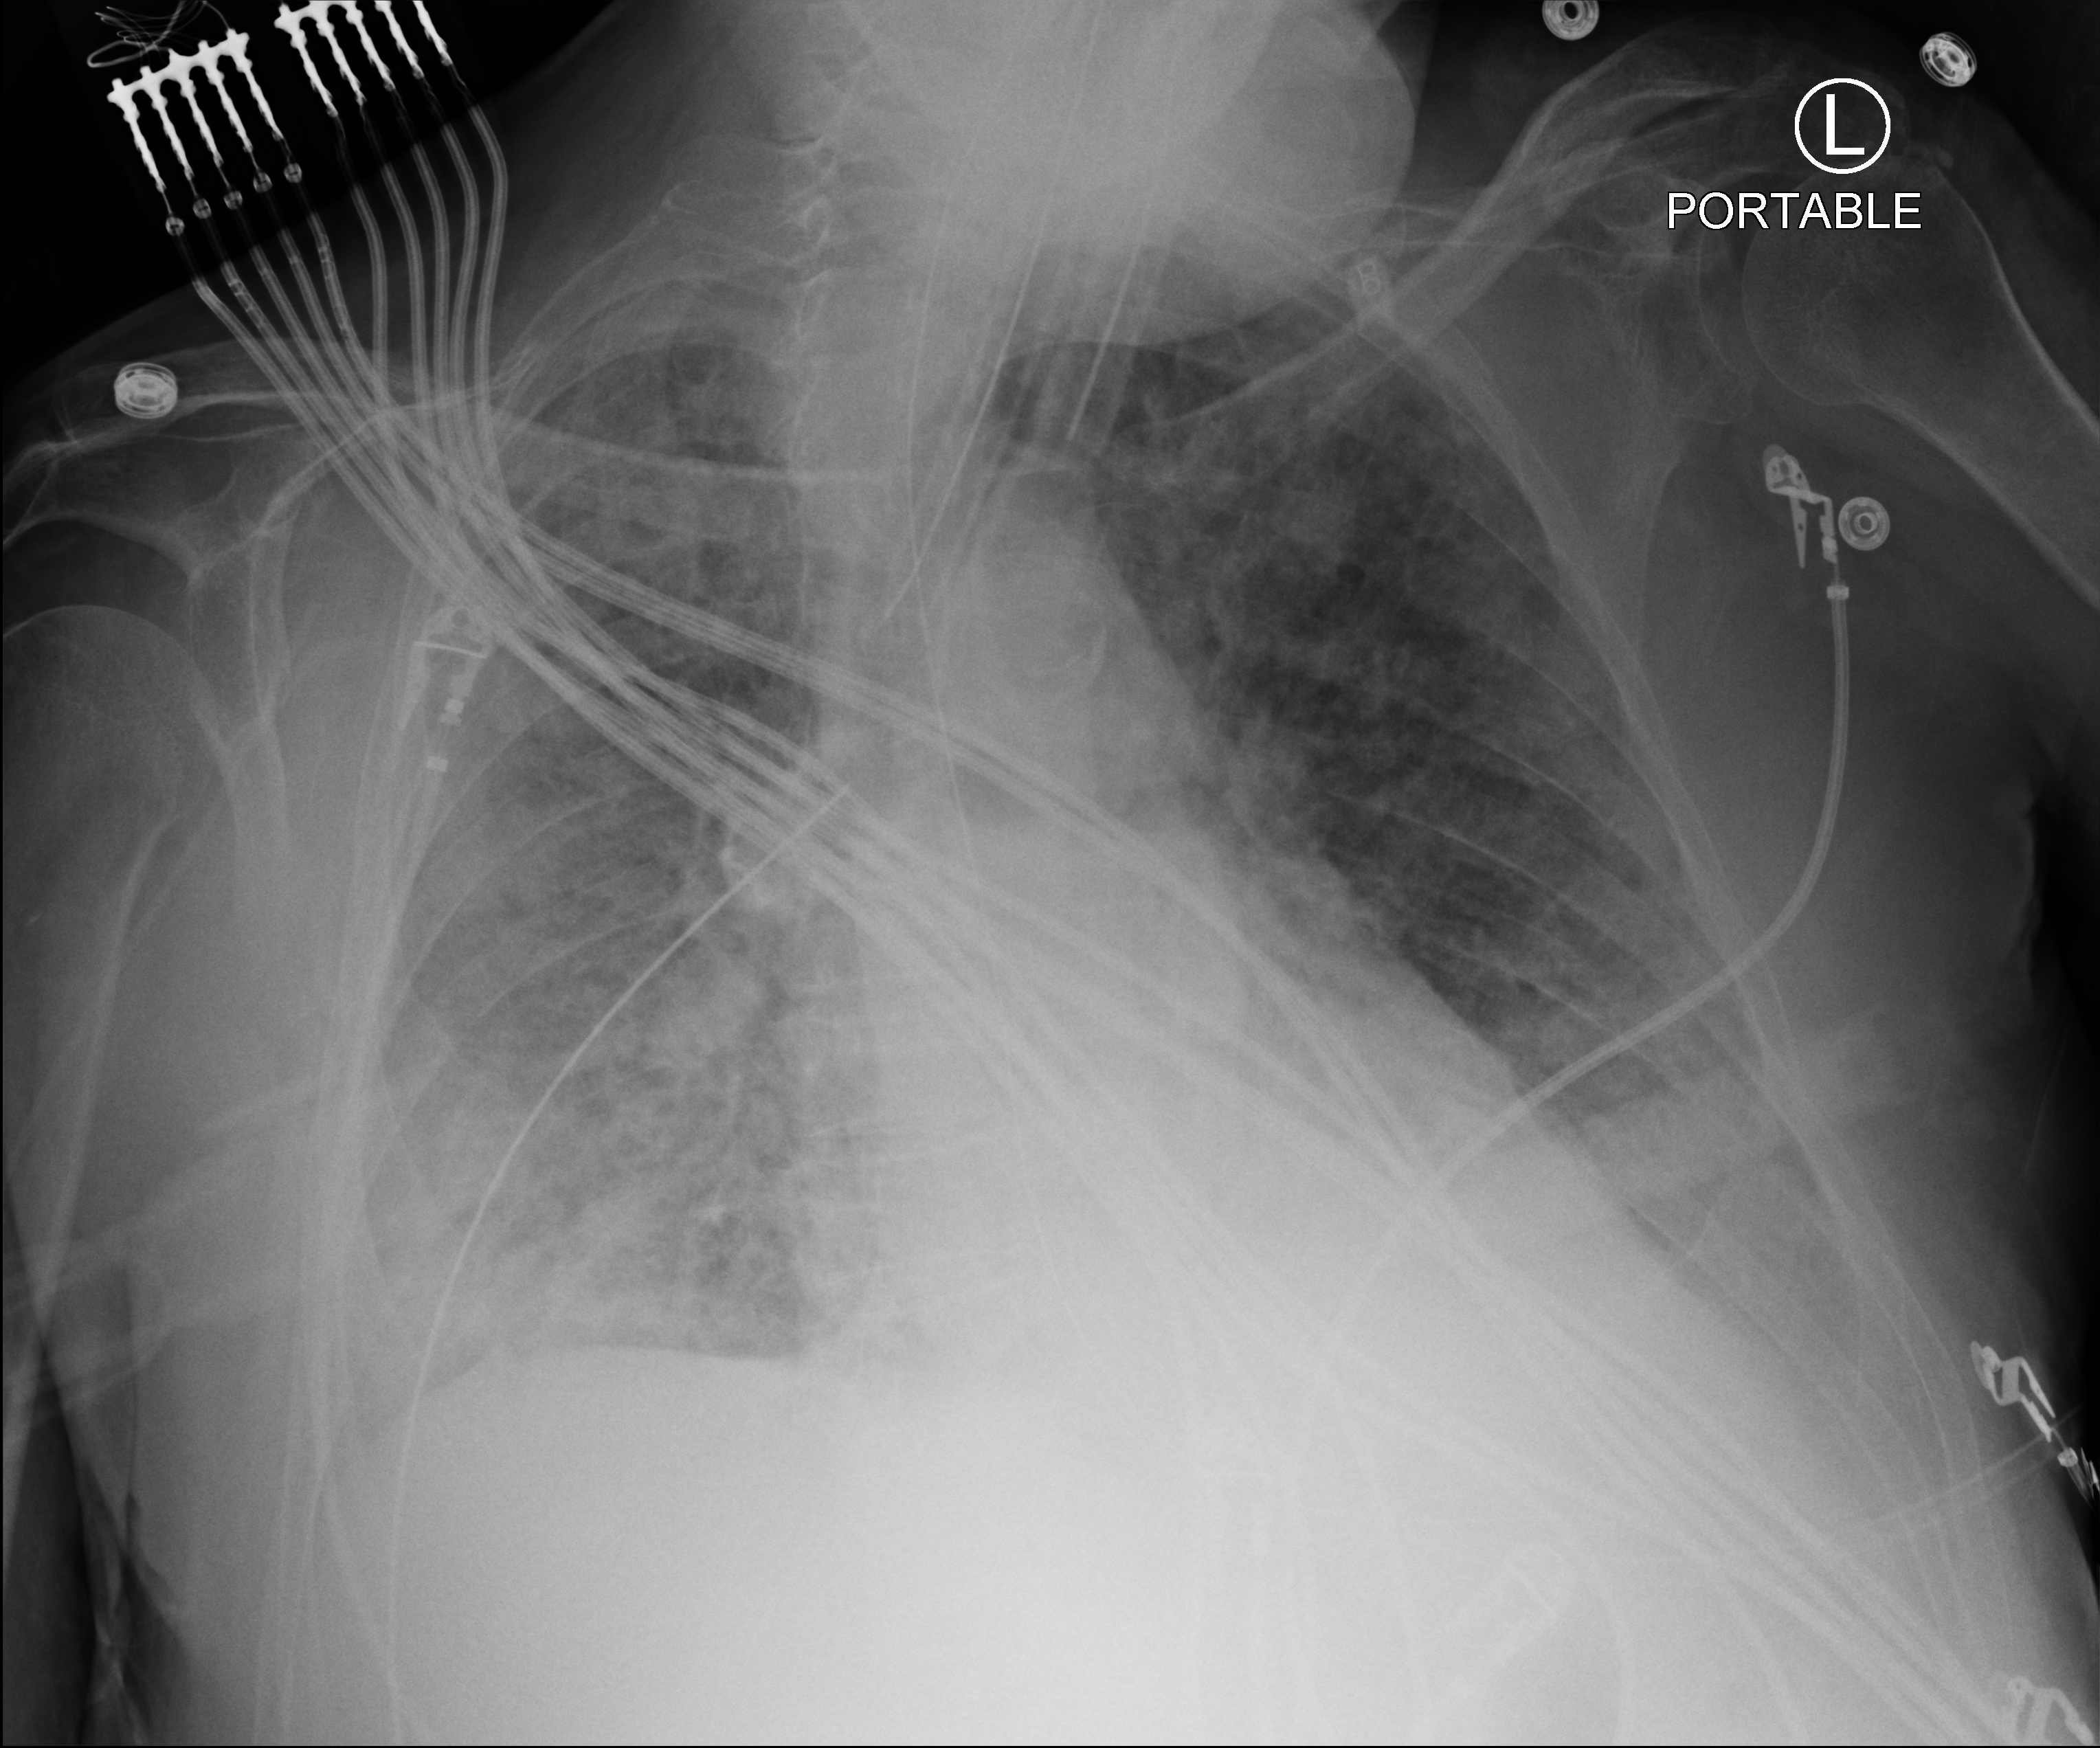
Chest X-ray (portable); anteroposterior (AP) projection. Patient hospitalised with COVID-19; male, aged 60–74 years.
Hospital-stay facts (about this admission, not read from this image; timing relative to this image not recorded): mechanically ventilated during this hospital stay: yes.